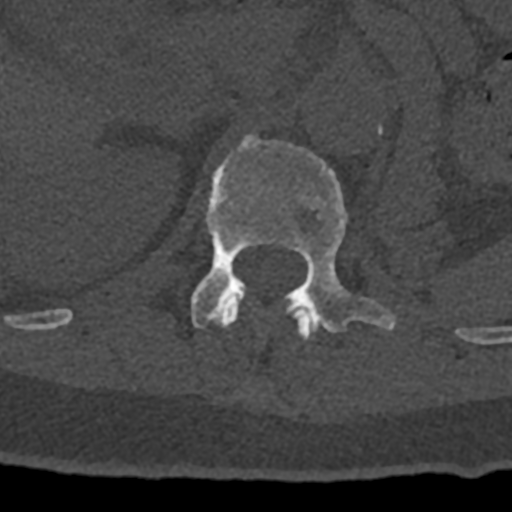
CT including the spine, one axial slice. Position 451 of 797 along the scan axis. Reconstruction kernel Br40s/3. 120 kVp. Bone window (W 1800 / L 400 HU). 0.5 mm slice thickness. 512 × 512 image matrix. Male patient, age 74 years. Case-level facts recorded for this patient, not image findings: primary cancer: renal; vertebrae with lytic lesions (as recorded): T10, L1, L2, L3, L4, L5.
Structures marked on this image (semi-automatically segmented with operator editing):
- L1 vertebra: bounding box (x1, y1, x2, y2) in pixels: (191, 134, 396, 333)
- T12 vertebra: (70, 298, 315, 340)